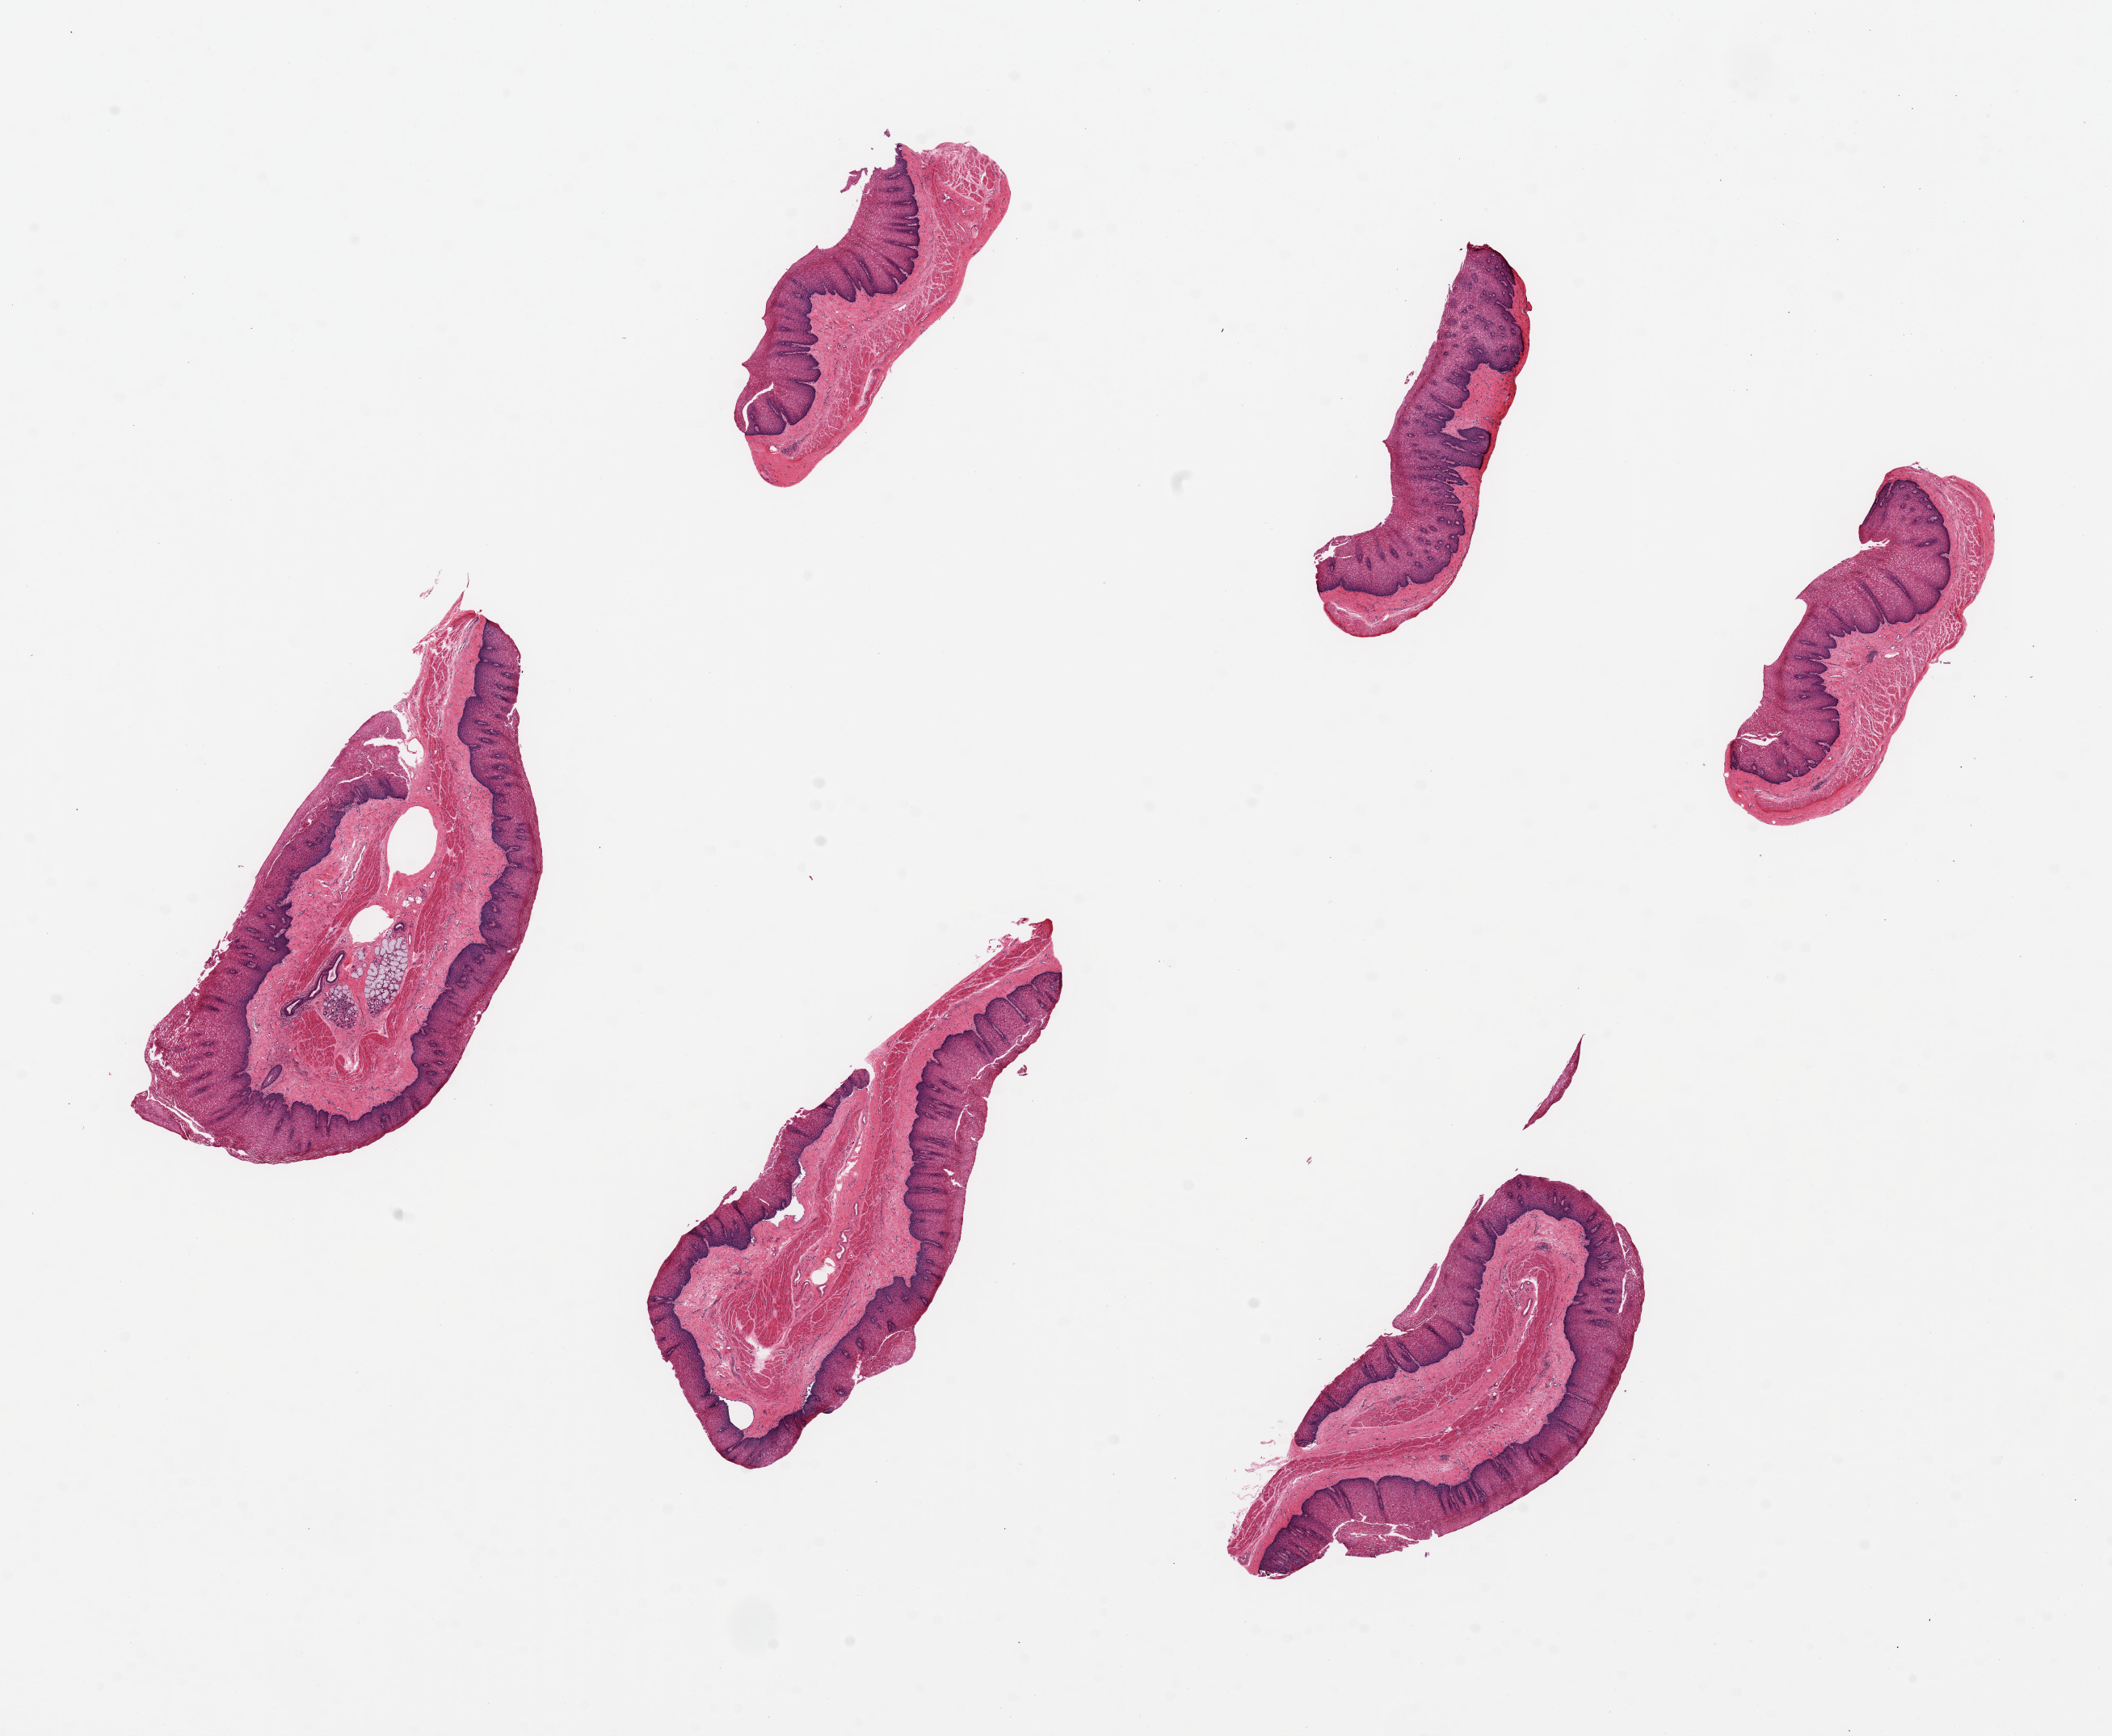
H&E whole-slide image — a low-resolution overview of the entire scanned area, about 20.7 x 17.0 mm. PAXgene-fixed paraffin-embedded (PFPE) section. Section of esophageal mucous membrane (target tissue). Donor tissue sample. Donor: male.
- reviewer comment on this tissue sample: 6 pieces ~6x1mm, Squamous mucosa is ~40-50% thickness